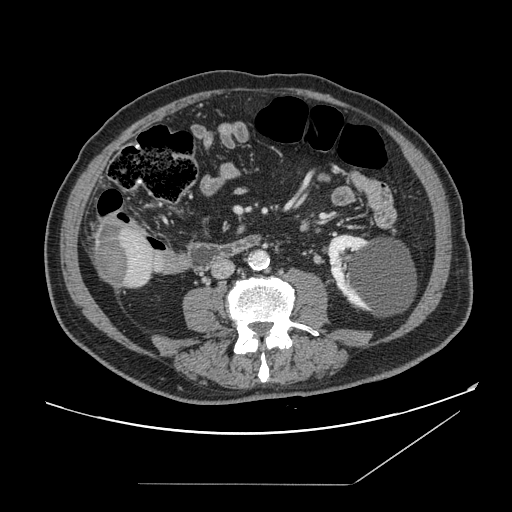
Contrast-enhanced abdominal CT, one axial slice; intravenous contrast given; soft-tissue window (W 400 / L 40 HU); 2.5 mm slice thickness; 512 × 512 image matrix, field of view 416 × 416 mm. Male patient, age 80 years. From the clinical record (not read from this slice): diagnosis: colorectal cancer liver metastases, imaged before liver resection; multiple liver metastases: no; largest metastasis: 2.2 cm; disease in both lobes: no.
Structures marked on this image (outlined manually by an expert reader):
- liver: box from (x=93, y=222) to (x=156, y=289) px
- liver metastasis: (x=97, y=226)–(x=131, y=287)